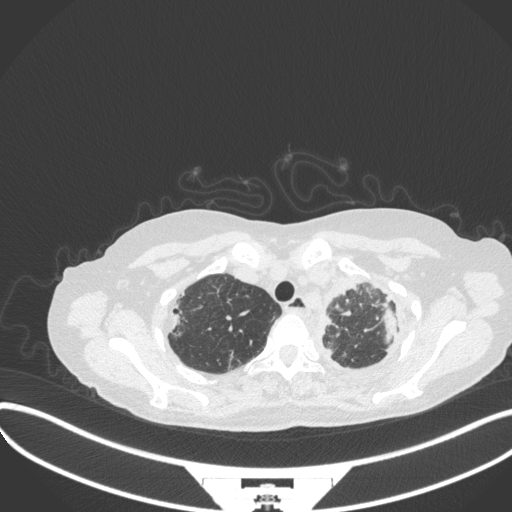
Chest CT, one axial slice. Position 291 of 373 along the scan axis. Reconstruction kernel B31f. Lung window (W 1500 / L -600 HU). 1 mm slice thickness. 512 × 512 image matrix, field of view 400 × 400 mm. Female patient, age 56 years. From the clinical record (not read from this slice): clinical TNM (as recorded): T1 N0 M0.
Structures marked on this image (bounding box drawn by a radiologist):
- lung tumour (recorded histology: adenocarcinoma): bounding box (x1, y1, x2, y2) in pixels: (381, 302, 396, 343)